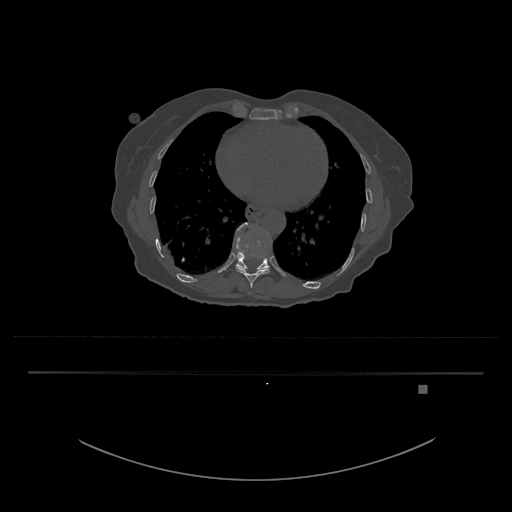
CT including the spine, one axial slice. Position 695 of 797 along the scan axis. Reconstruction kernel Br40s/3. 120 kVp. Bone window (W 1800 / L 400 HU). 512 × 512 image matrix, field of view 500 × 500 mm. Patient: female, 57 years. Case-level facts recorded for this patient, not image findings: primary cancer: cervical.
Outlined on this slice (semi-automatic segmentation, software-assisted and operator-edited):
- T10 vertebra: bounding box (x1, y1, x2, y2) in pixels: (236, 268, 270, 288)
- T11 vertebra: (233, 222, 270, 270)